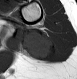
MRI of an extremity soft-tissue mass, one axial slice; position 12 of 28 along the scan axis; MR volume resampled by the dataset authors to the PET/CT grid (not the native acquisition matrix); 3.27 mm slice thickness; 77 × 79 image matrix. Female patient. Case-level facts recorded for this patient, not image findings: histological type: malignant fibrous histiocytoma; grade: low; site of the primary tumour: left arm.
Annotated regions visible in this slice (expert contour drawn on MRI and transferred to this co-registered scan by the dataset authors):
- gross tumour volume (mass): bounding box (x1, y1, x2, y2) in pixels: (19, 27, 57, 62)